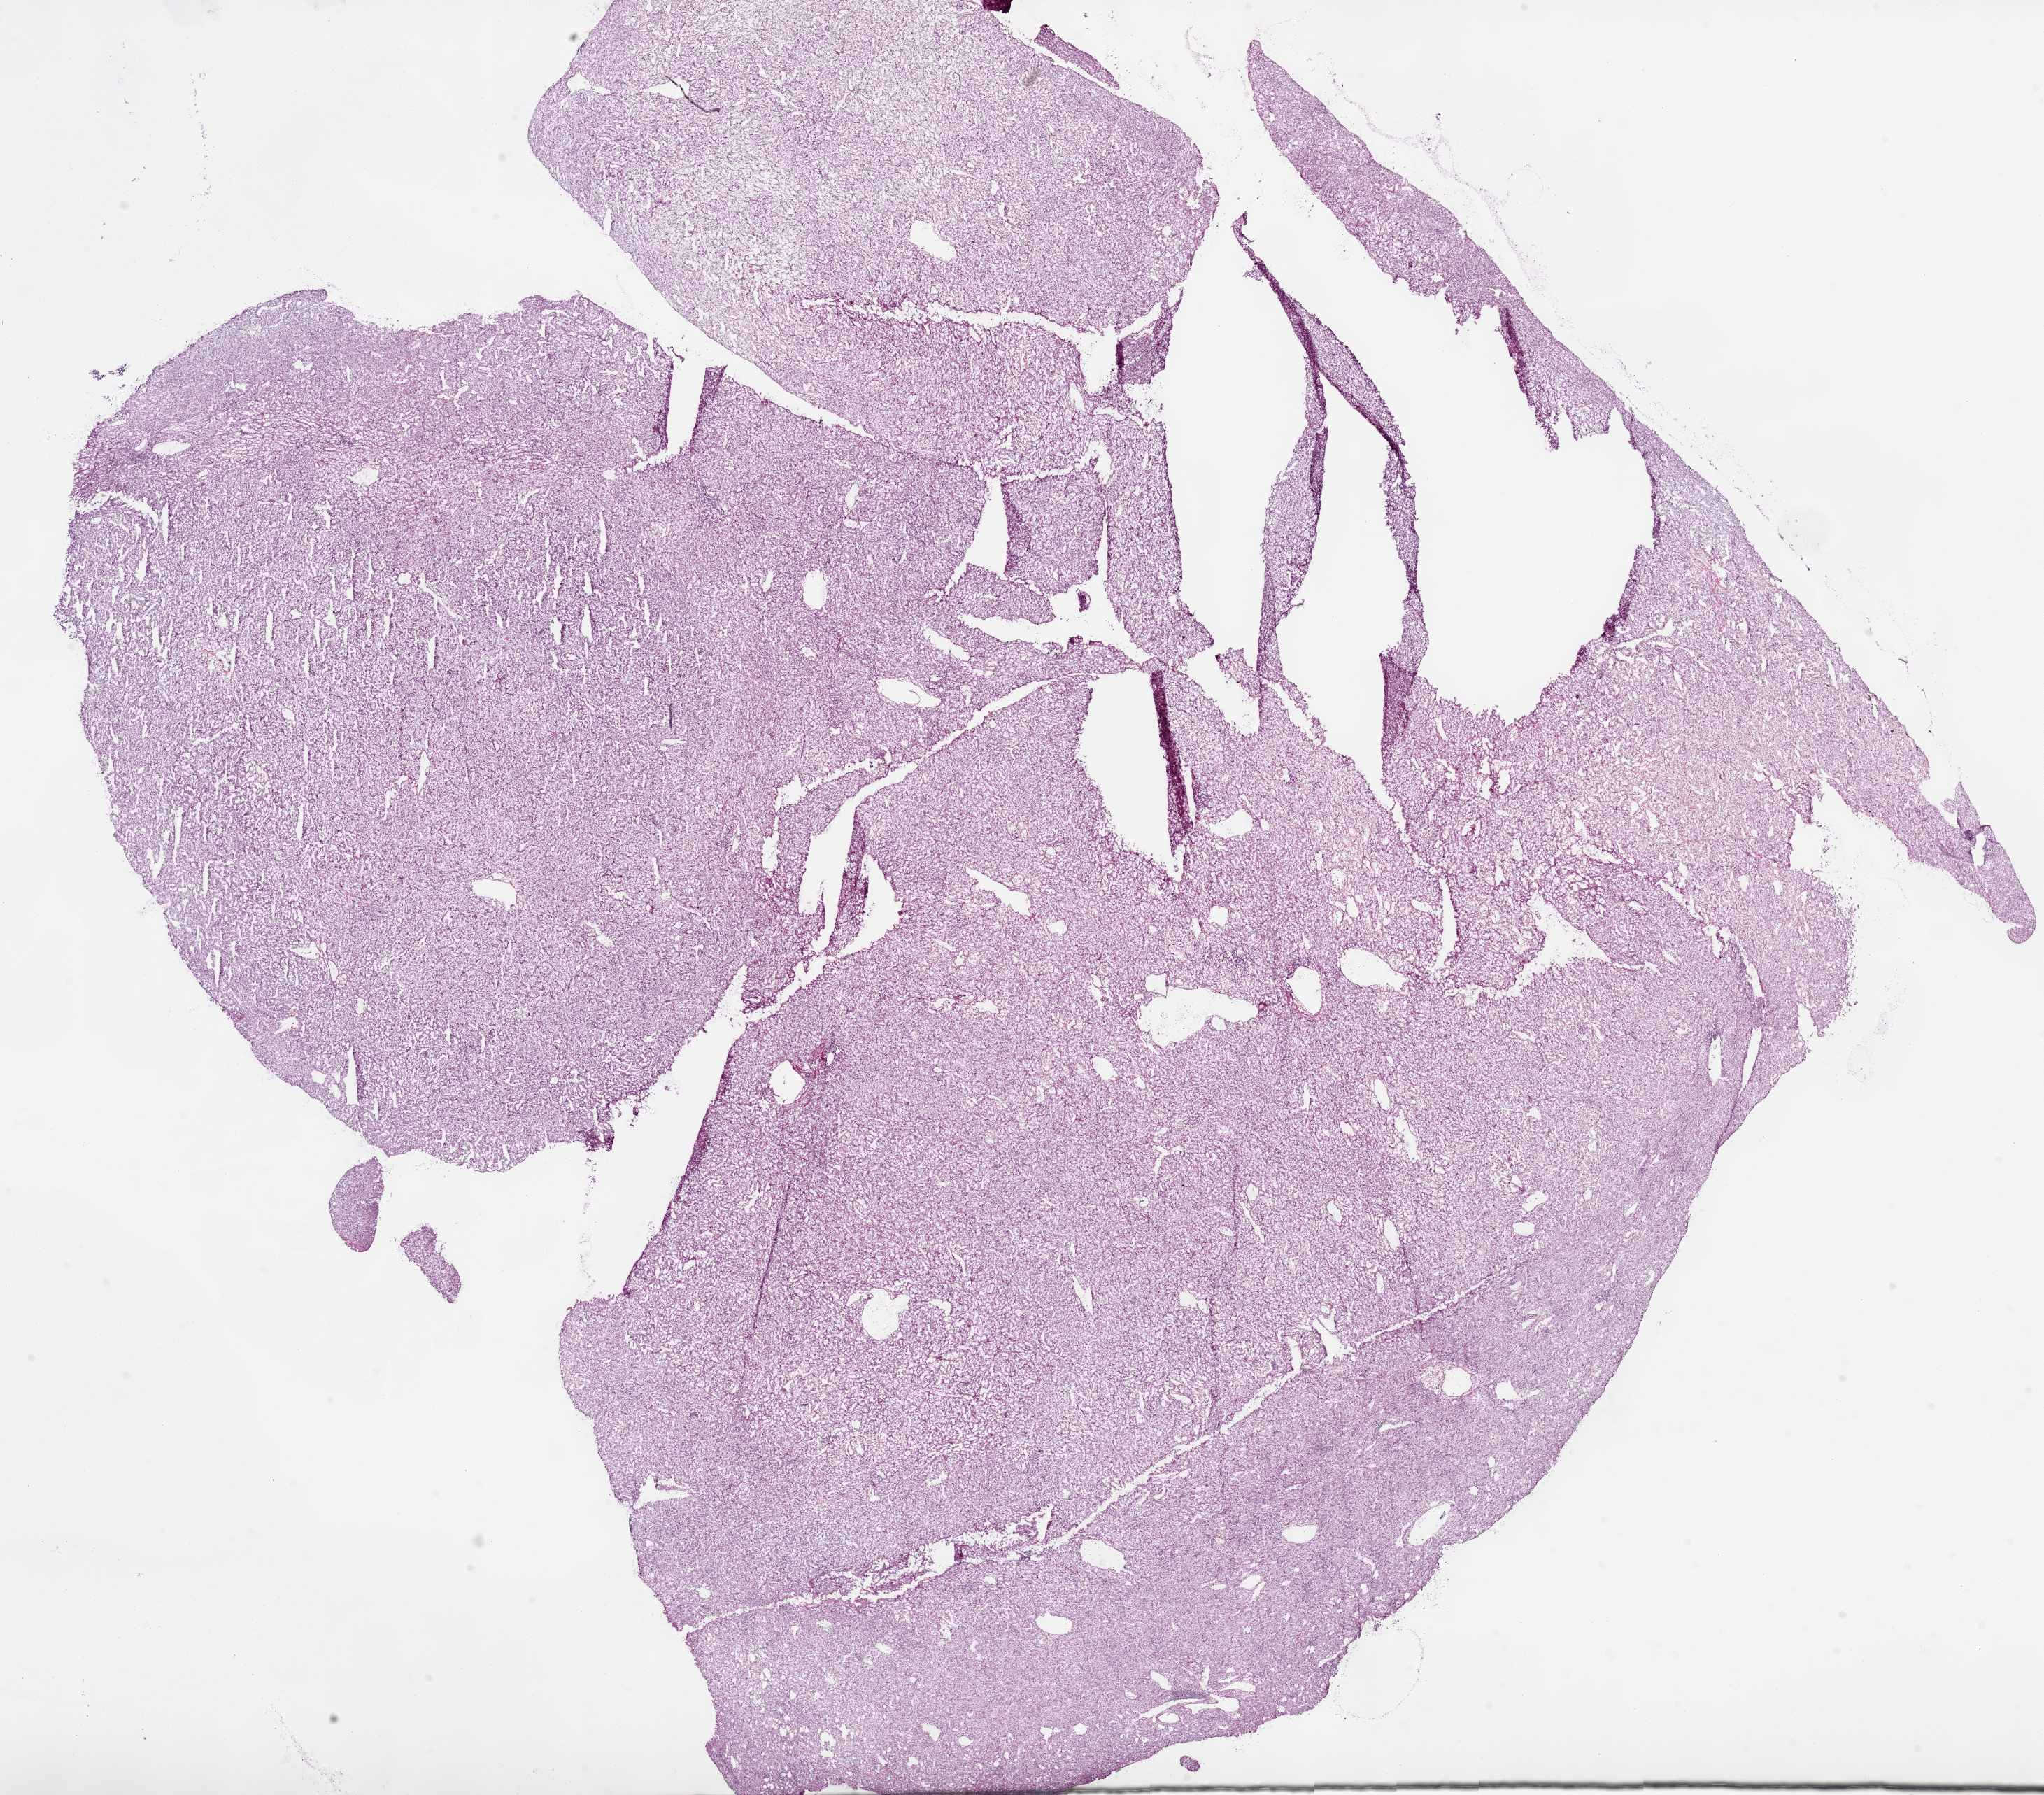
Whole-slide histology image, H&E — whole scanned area (about 23.4 x 20.6 mm, slide scanned at 5x) shown as a low-resolution overview. Frozen section from the bottom of the tissue portion. Sample: primary tumour, kidney. Male patient; age at initial diagnosis 46 years. Histologic grade: G2 (moderately differentiated). Pathologist review of this section (percent, as recorded): tumour cells 97%, tumour nuclei 85%, normal cells 0%, stromal cells 3%, necrosis 0%.
* AJCC pathologic stage: I (7th edition)
* TNM: T1b N0 M0
* laterality: right
* diagnosis: Clear cell adenocarcinoma, NOS